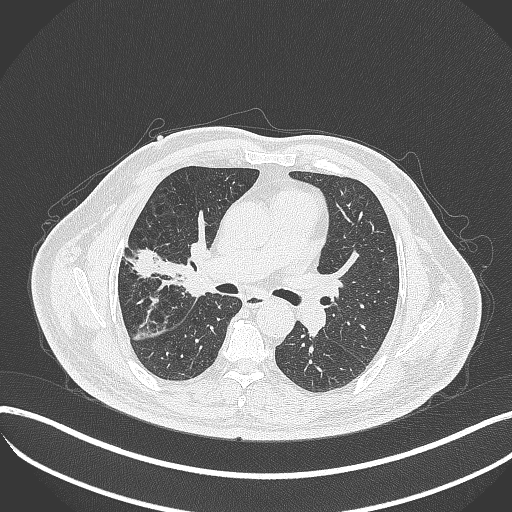
Chest CT, one axial slice; slice 209 of 401 in the series (ordered by position); 120 kVp; lung window (W 1500 / L -600 HU); 1 mm slice thickness; 512 × 512 image matrix, field of view 400 × 400 mm. Patient: male, 72 years. From the clinical record (not read from this slice): clinical TNM (as recorded): T1c N0 M0.
Outlined on this slice (bounding box drawn by a radiologist):
- lung tumour (recorded histology: squamous cell carcinoma): box from (x=172, y=236) to (x=222, y=307) px